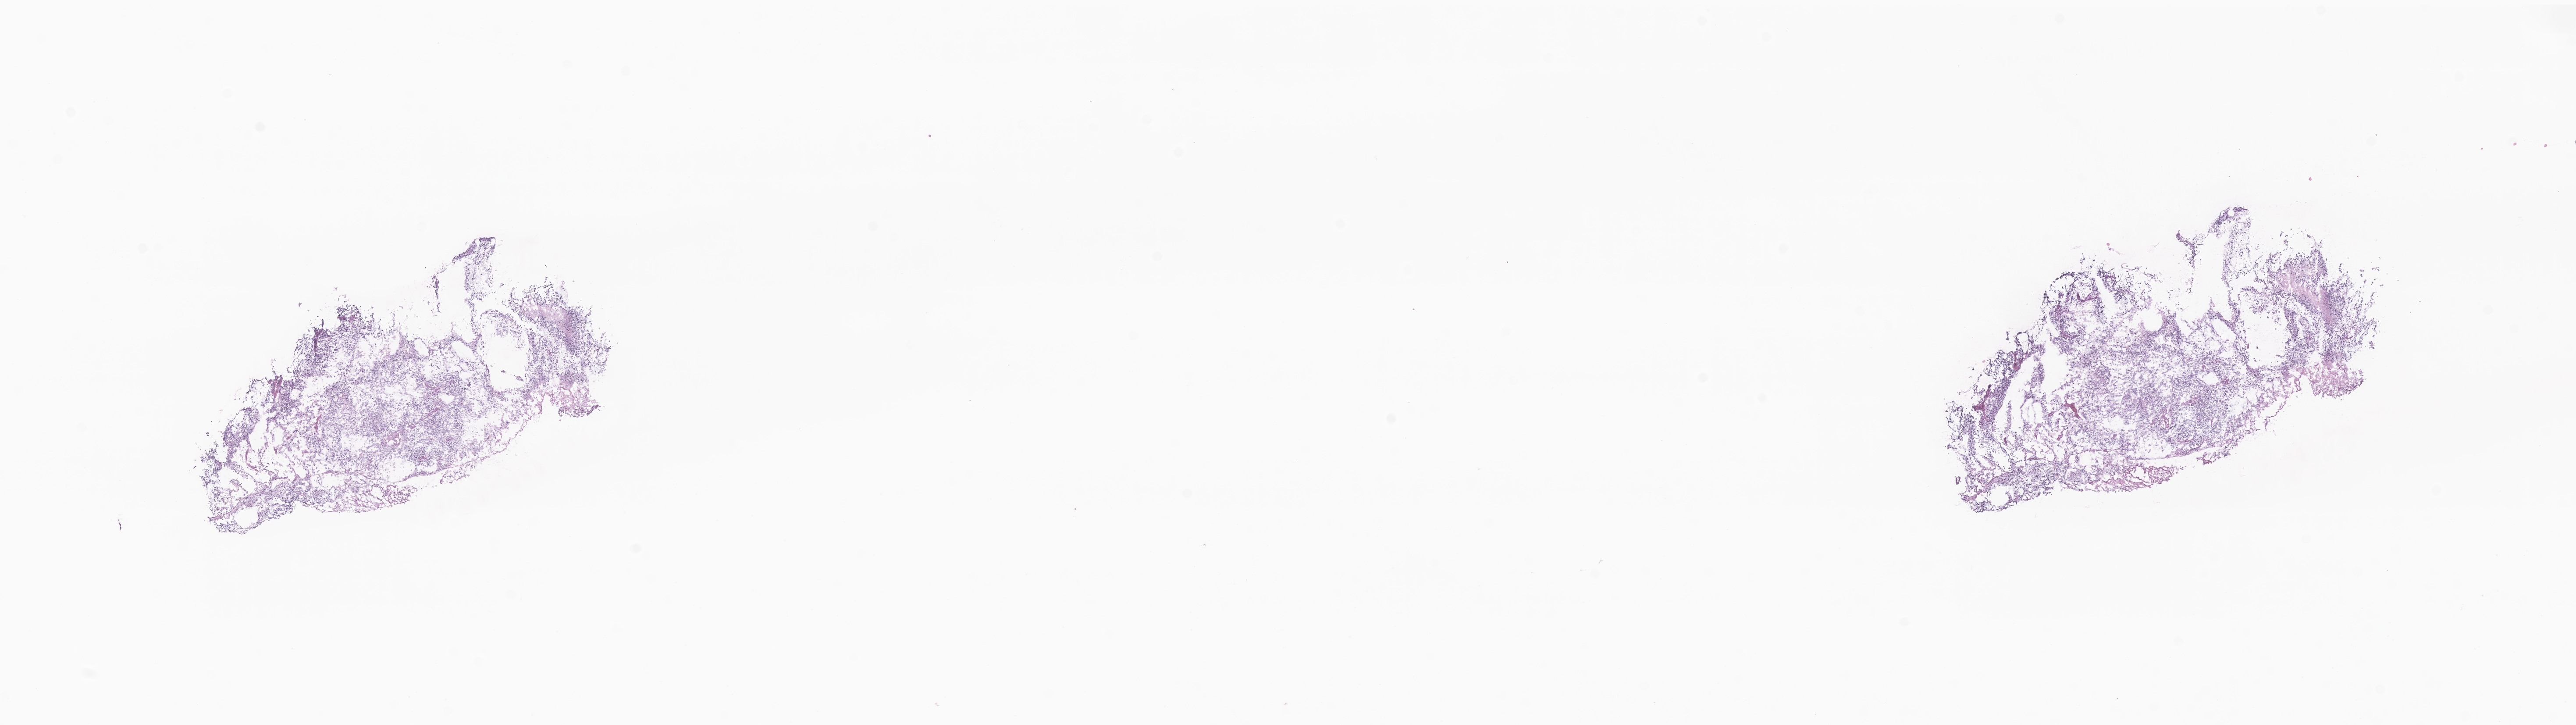
Digitized hematoxylin and eosin (H&E)-stained section of tumor tissue from the brain — whole scanned area (about 24.8 x 7.0 mm) shown as a low-resolution overview. Female patient, age 83 months (6 years 11 months).
Specimen: frozen section (OCT-embedded).